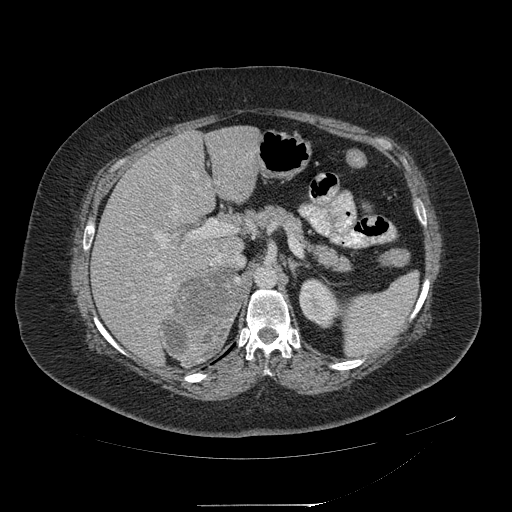
Contrast-enhanced abdominal CT, one axial slice; 120 kVp; soft-tissue window (W 400 / L 40 HU); 512 × 512 image matrix, field of view 453 × 453 mm. Female patient, age 55 years. Case-level facts recorded for this patient, not image findings: diagnosis: adrenocortical carcinoma; tumour side: right adrenal; tumour size at pathology: 11 cm; Ki-67 index: 20 %.
Structures marked on this image (semi-automatic segmentation, software-assisted and operator-edited):
- mass: box from (x=162, y=272) to (x=241, y=365) px